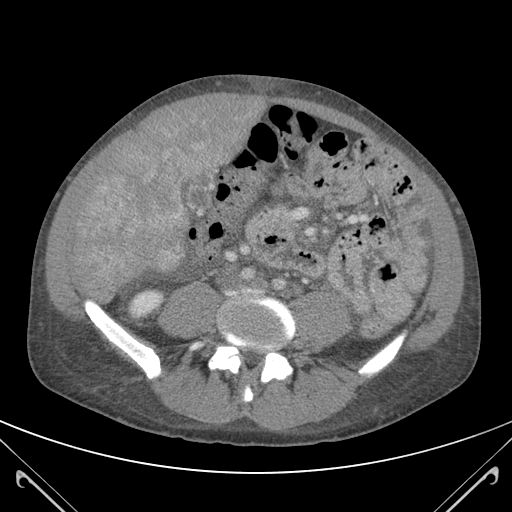
Contrast-enhanced abdominal CT (liver protocol), one axial slice. Position 31 of 118 along the scan axis. 120 kVp. Soft-tissue window (W 400 / L 40 HU). 3 mm slice thickness. 512 × 512 image matrix, field of view 380 × 380 mm. Case-level facts recorded for this patient, not image findings: diagnosis: hepatocellular carcinoma (patient treated with transarterial chemoembolisation; whether this scan precedes or follows treatment is not stated here); TNM stage (as recorded): Stage-IIIB; Child-Pugh class: A.
Outlined on this slice (semi-automatically segmented with operator editing):
- mass: bounding box (x1, y1, x2, y2) in pixels: (76, 95, 247, 277)